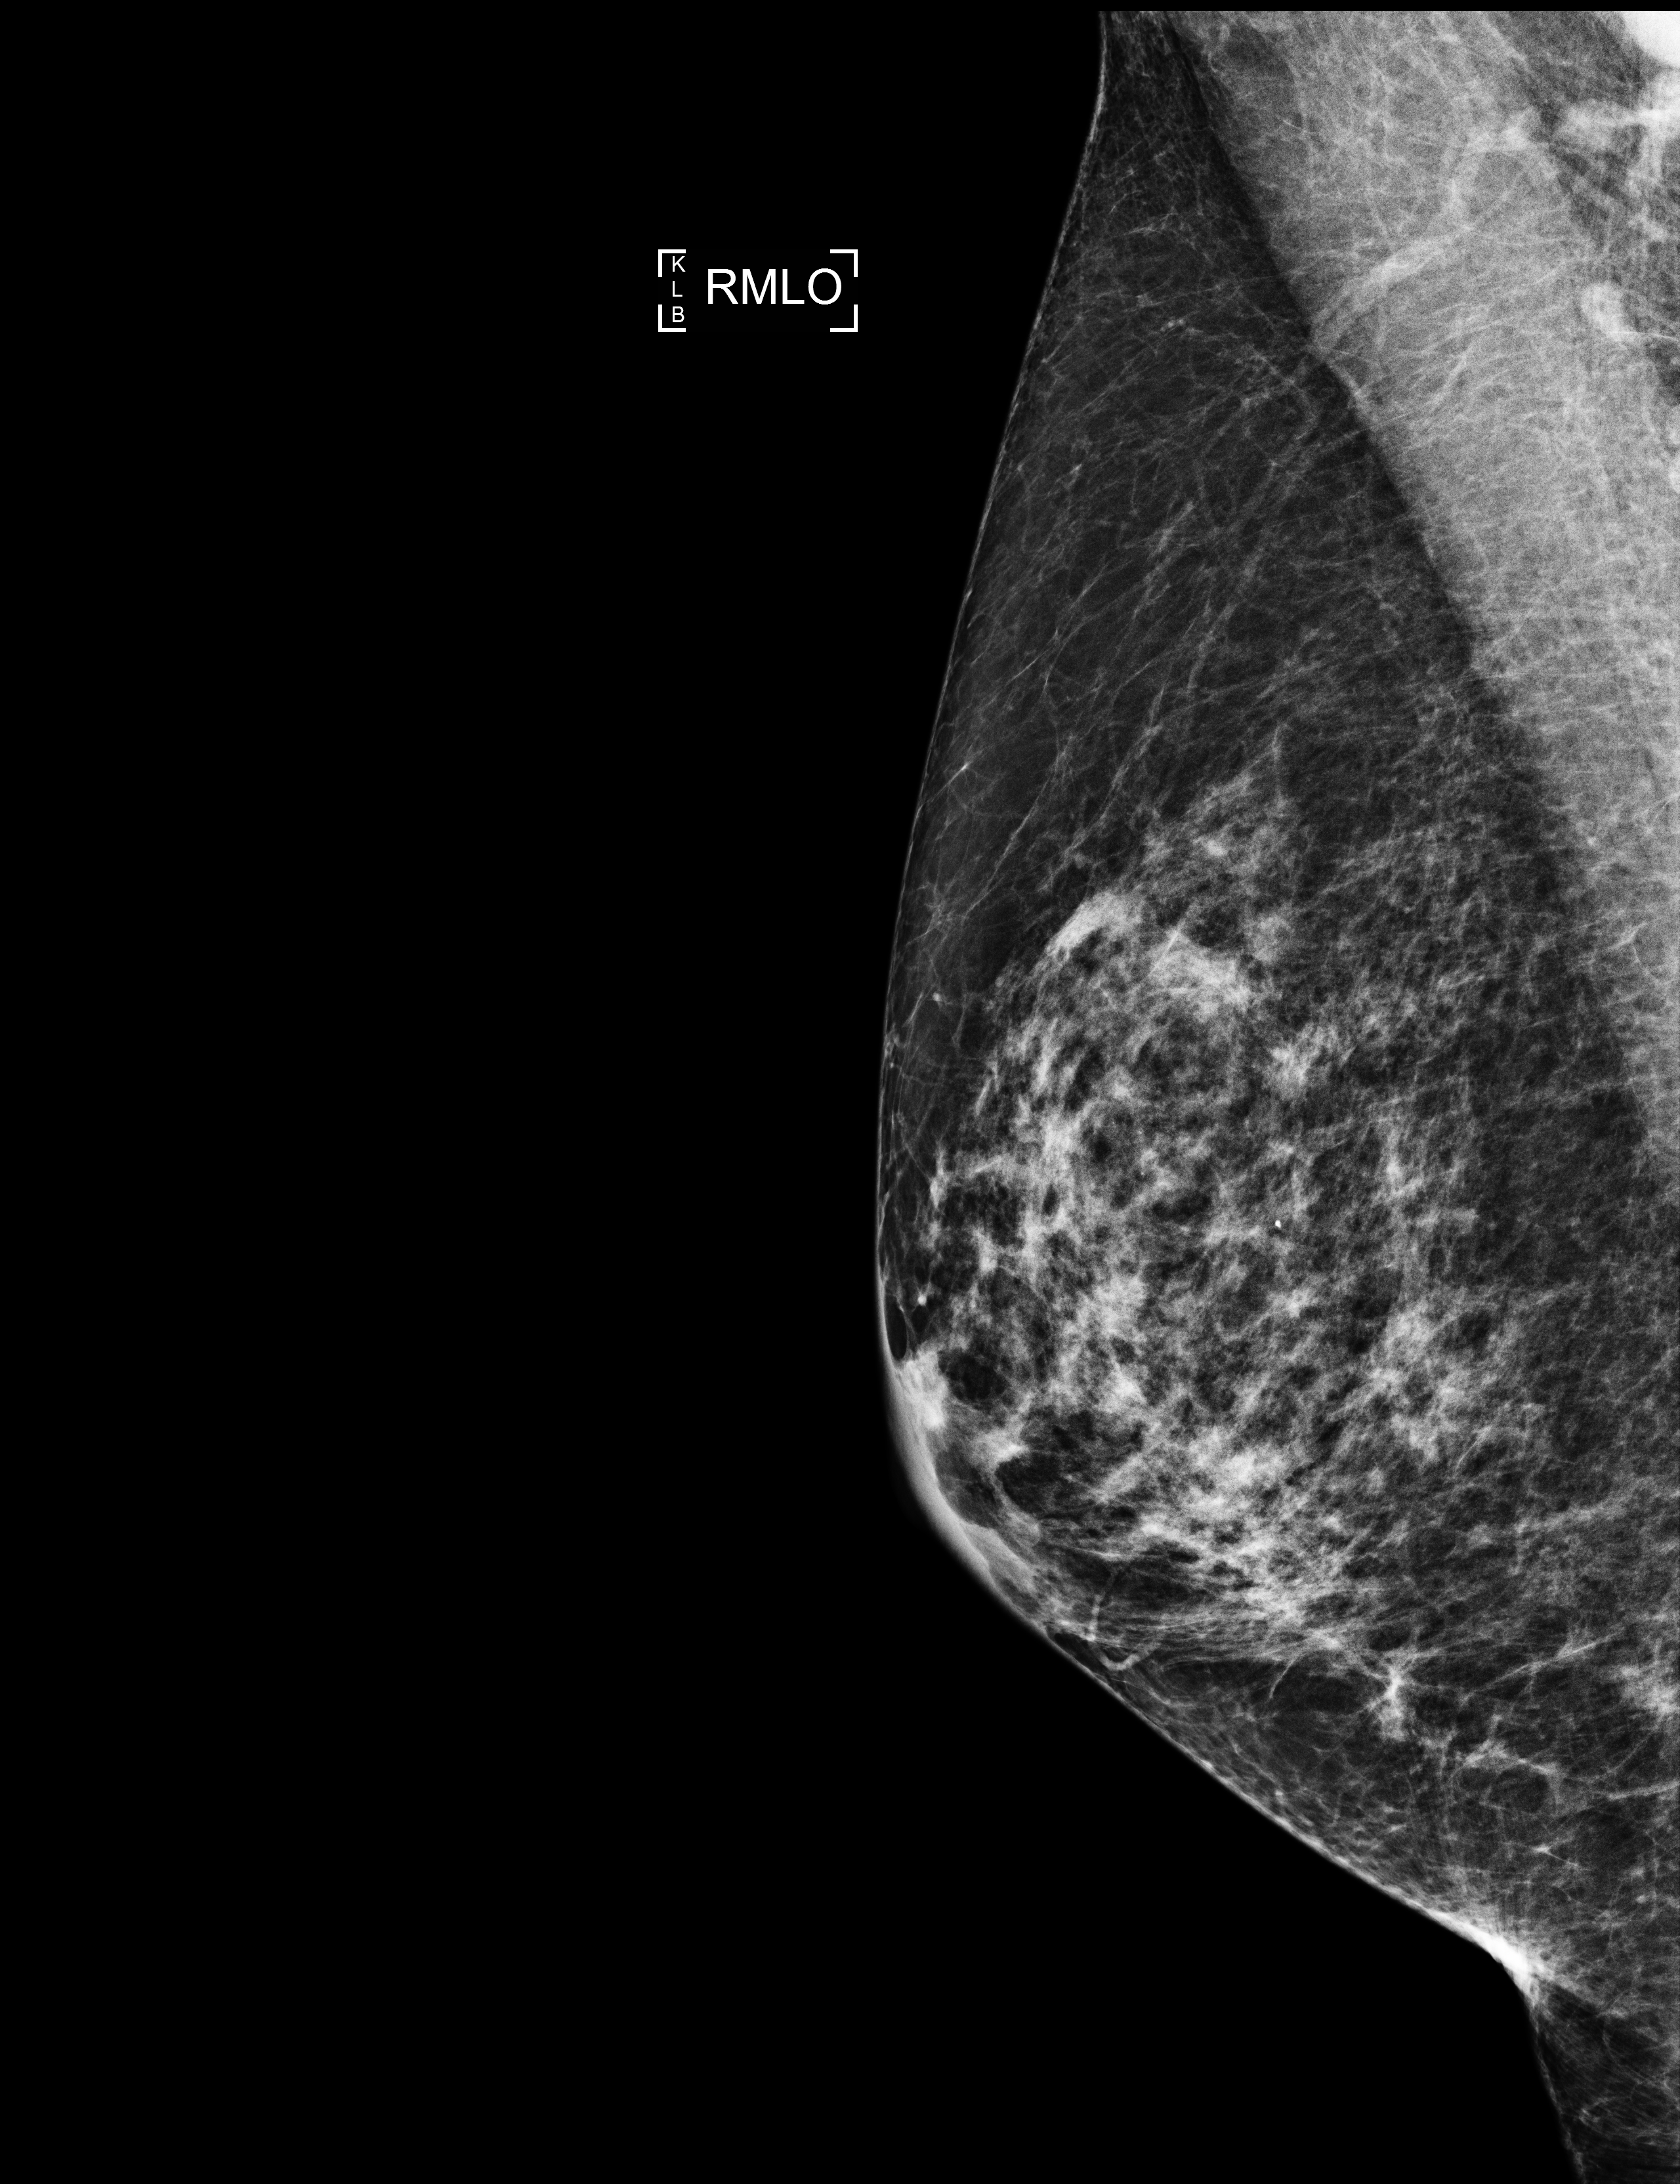
Screening examination. Female patient, age 64 years.
Image type: full-field digital mammogram. Breast: right. Projection: MLO view.